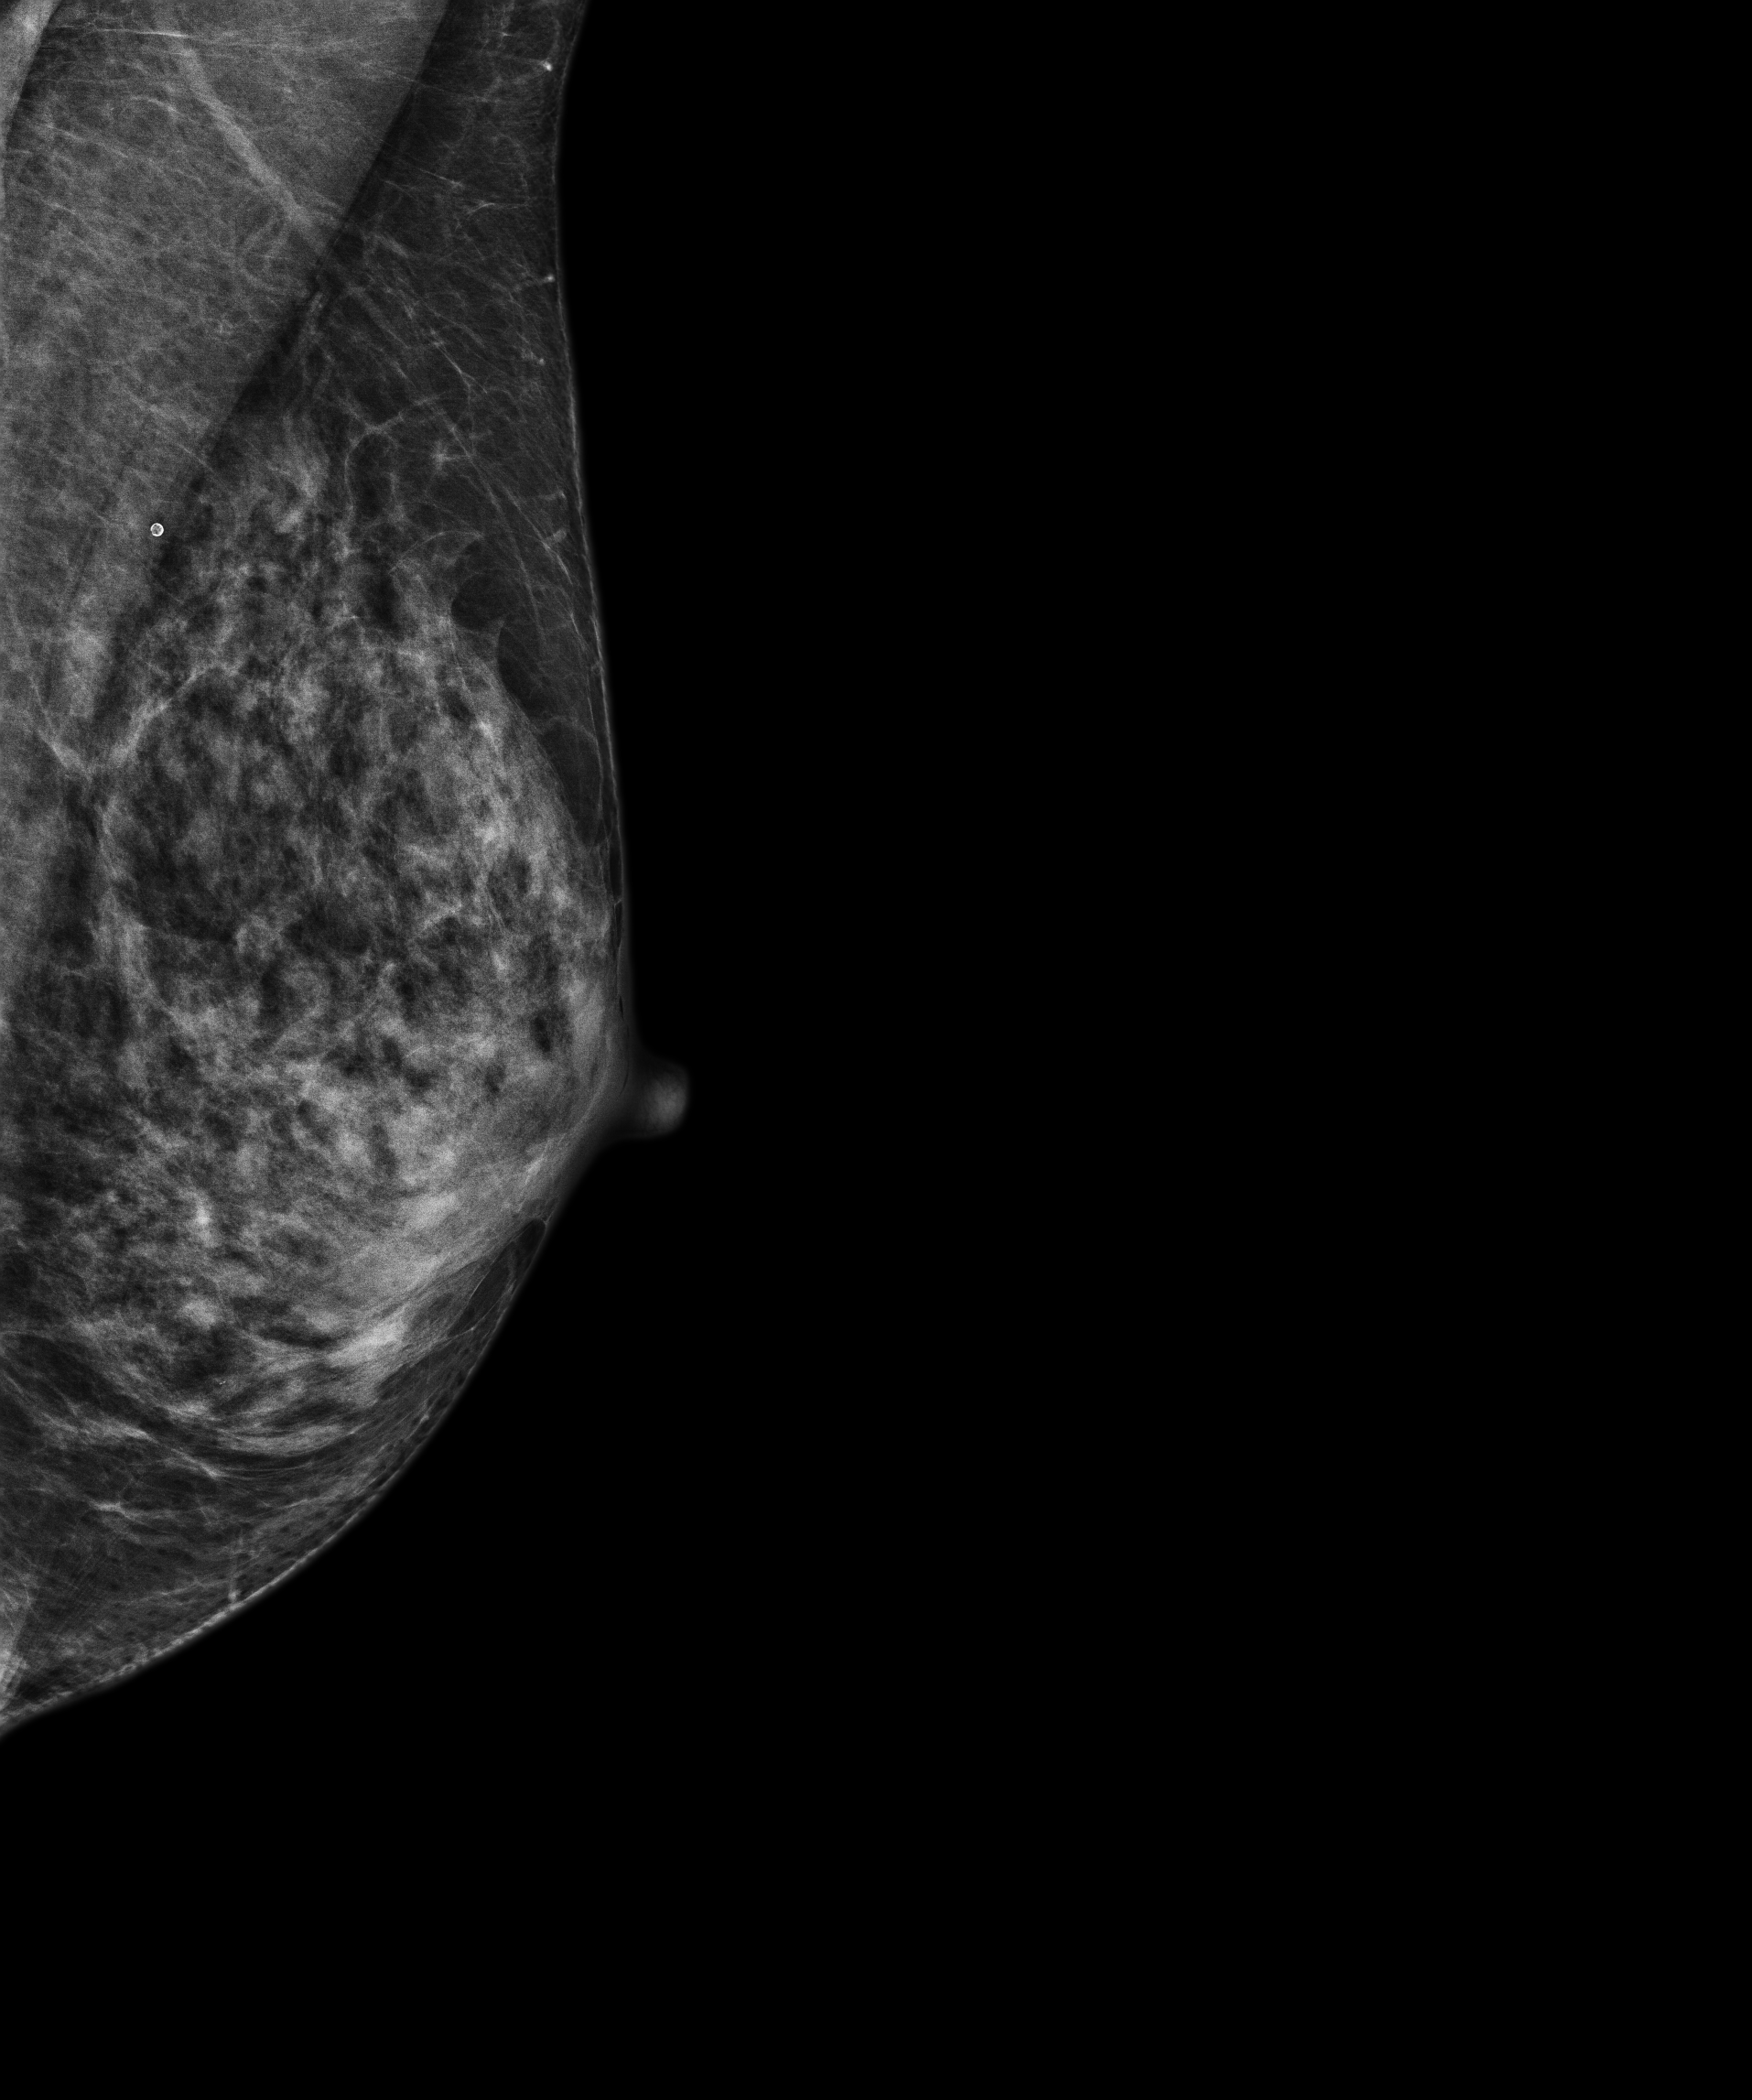
Annual screening mammography examination; compressed breast thickness 36.5 mm. Female patient, age 68 years.
Image type: full-field digital mammogram. Breast: left. Projection: MLO view.